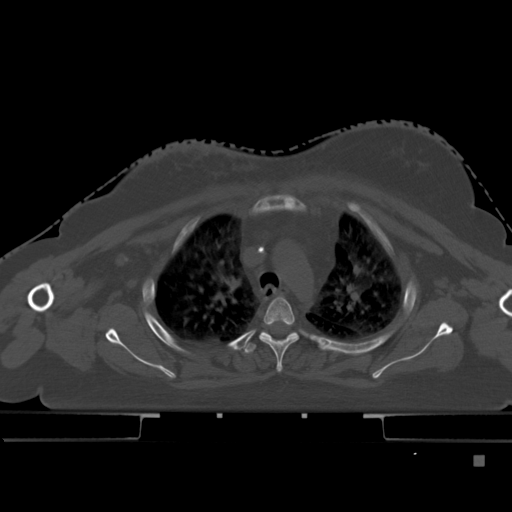
CT including the spine, one axial slice. Position 342 of 495 along the scan axis. Bone window (W 1800 / L 400 HU). 1.5 mm slice thickness. 512 × 512 image matrix, field of view 404 × 404 mm. Patient: female, 33 years. From the clinical record (not read from this slice): primary cancer: breast.
Structures marked on this image (semi-automatic segmentation, software-assisted and operator-edited):
- T3 vertebra: bounding box <260,297,299,373> (left, top, right, bottom; pixels)
- T4 vertebra: <244,331,300,354>